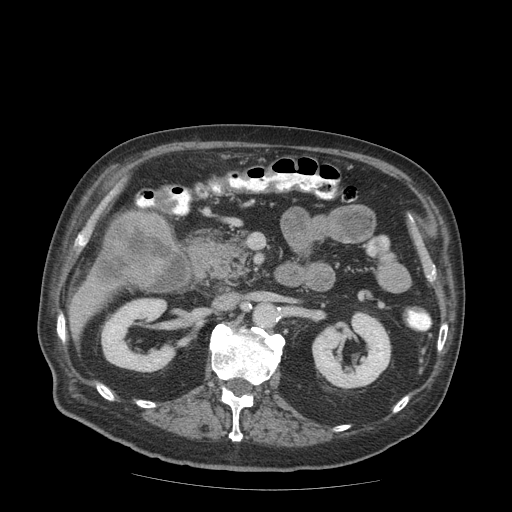
Contrast-enhanced abdominal CT (liver protocol), one axial slice; slice 26 of 99 in the series (ordered by position); reconstruction kernel STANDARD; 140 kVp; soft-tissue window (W 400 / L 40 HU); 512 × 512 image matrix. From the clinical record (not read from this slice): diagnosis: hepatocellular carcinoma (patient treated with transarterial chemoembolisation; whether this scan precedes or follows treatment is not stated here); TNM stage (as recorded): Stage-IIIB; Child-Pugh class: A; tumour differentiation: well differentiated; tumour nodularity: multinodular.
Structures marked on this image (semi-automatic segmentation, software-assisted and operator-edited):
- liver parenchyma outside the tumour (the mass and vessels are separate outlines, so this box may not span the whole liver): box from (x=72, y=321) to (x=82, y=337) px
- mass: (x=94, y=211)–(x=176, y=287)